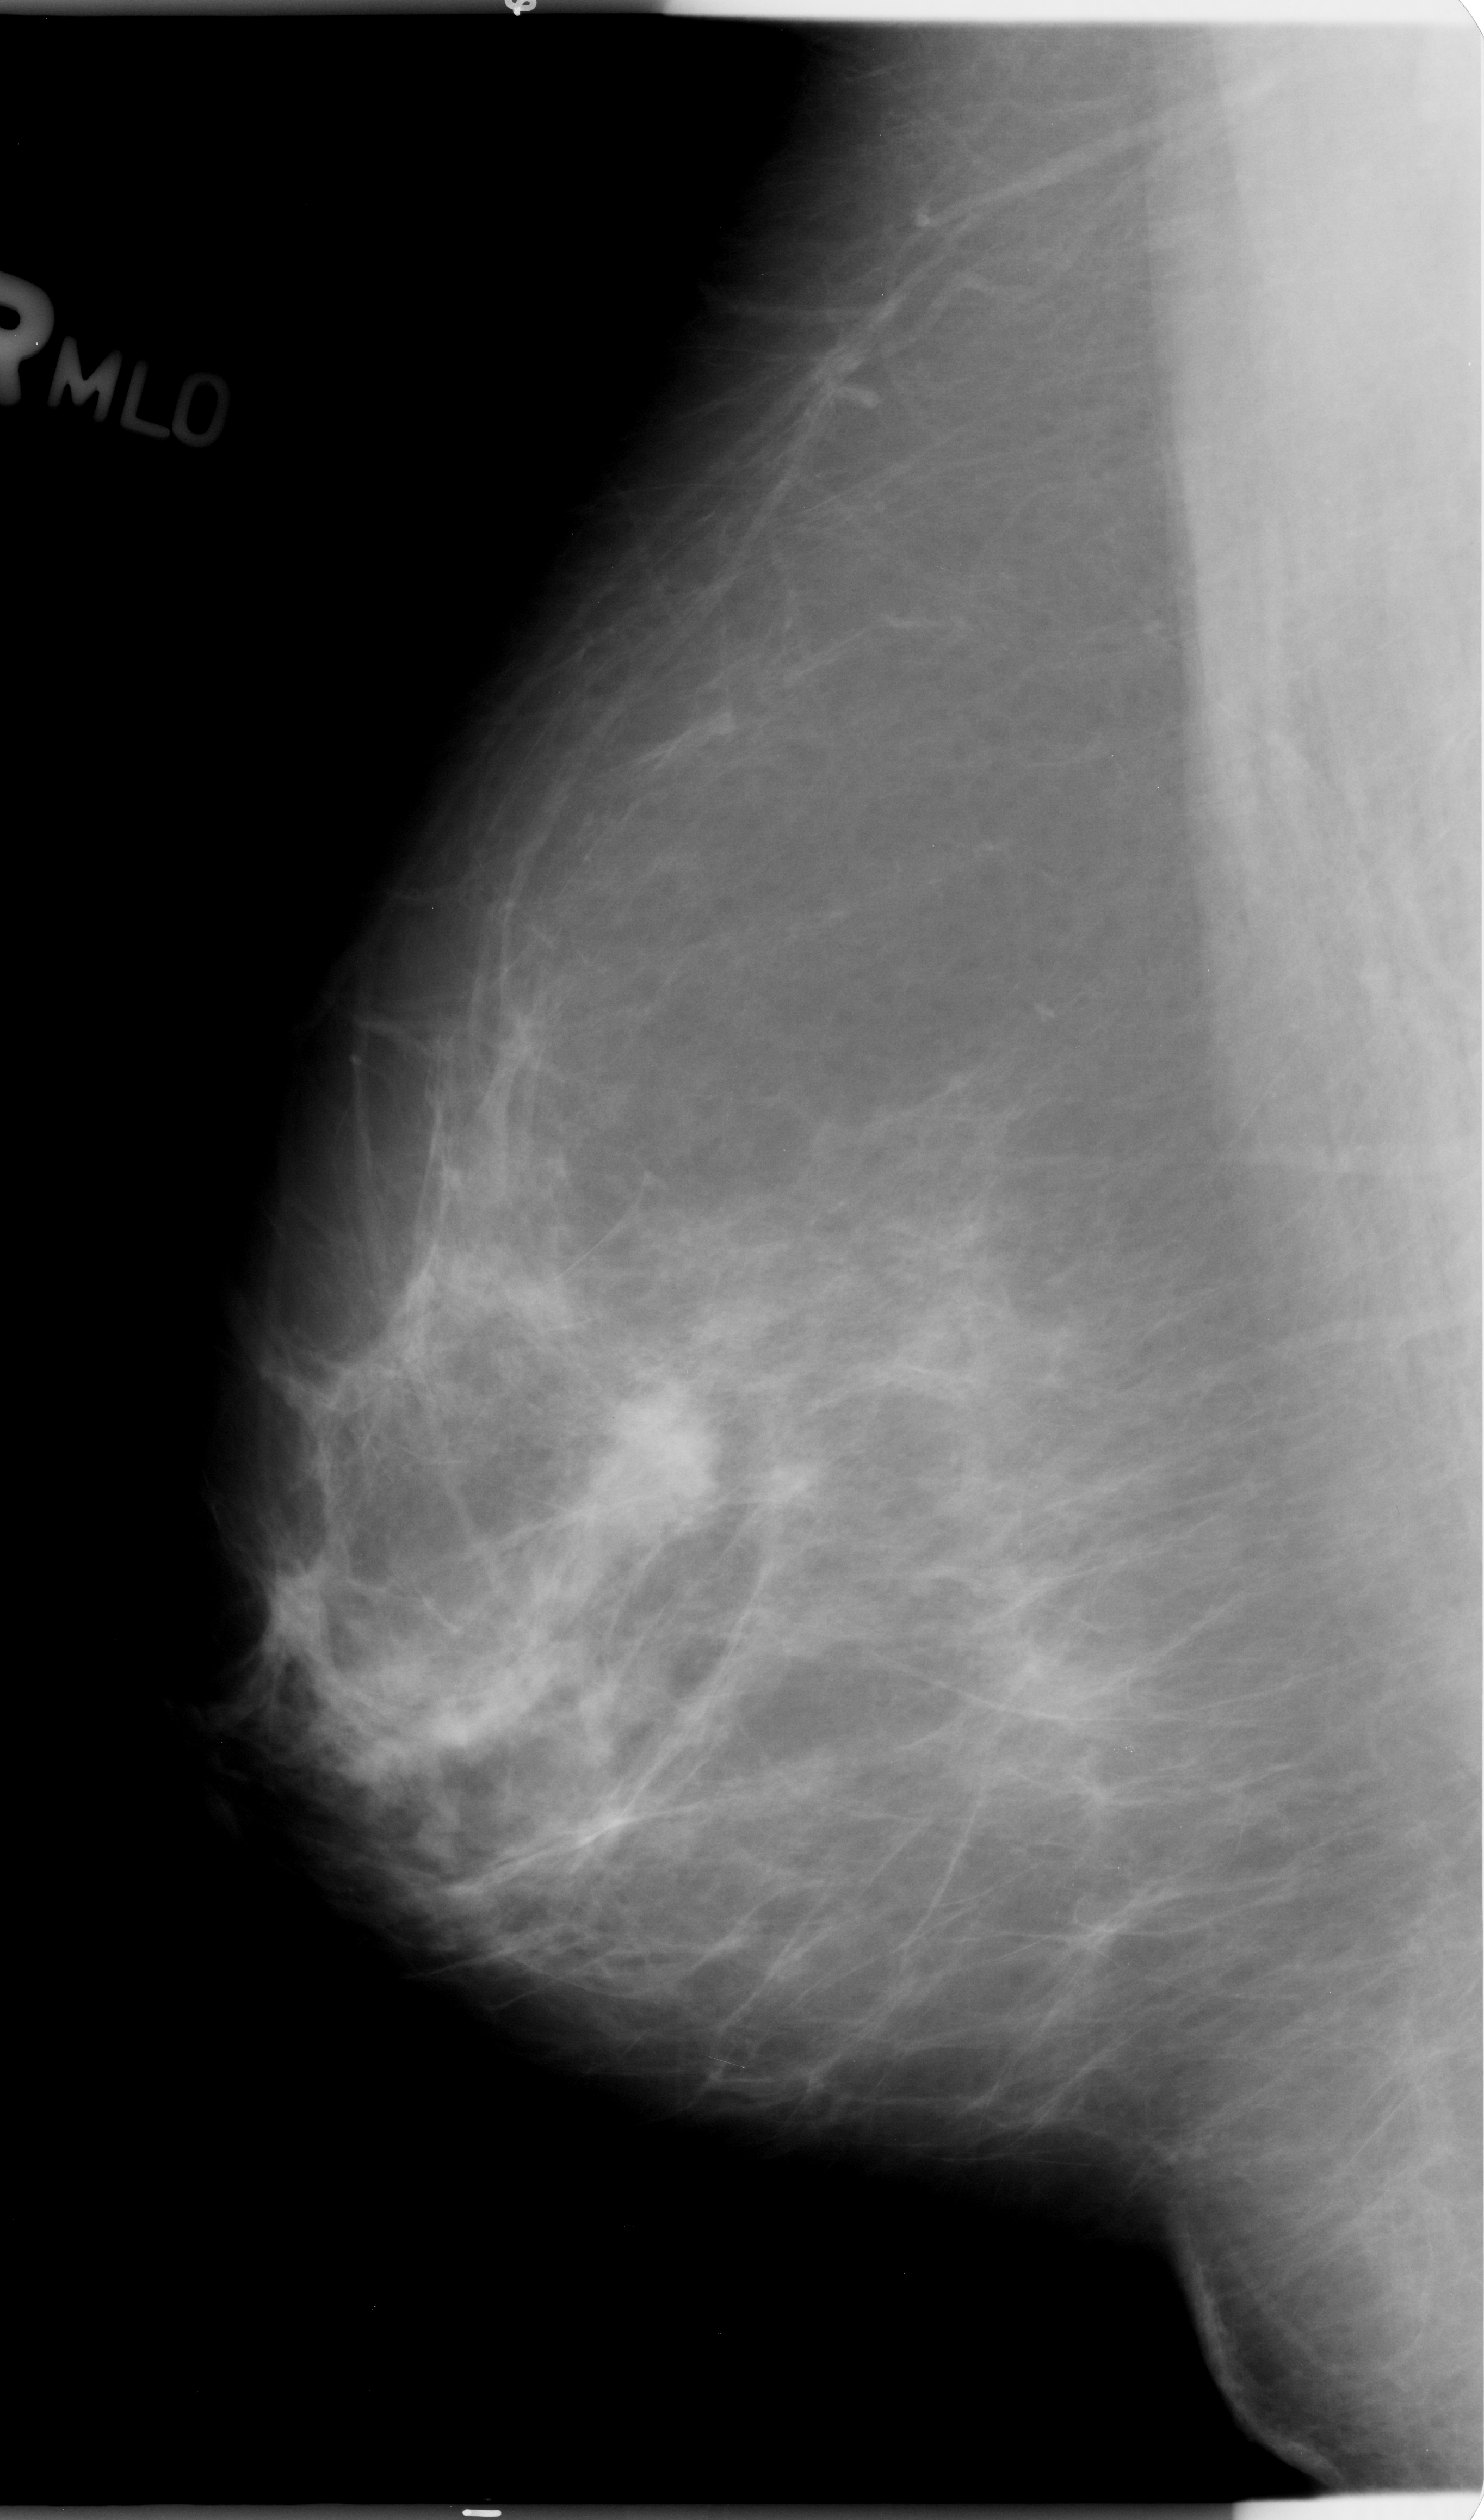
Digitized screen-film mammogram; right breast; mediolateral oblique (MLO) view; breast composition: scattered fibroglandular densities (BI-RADS density category 2 of 4).
Marked findings (only marked abnormalities are described; nothing is implied about the rest of the image): mass, shape irregular, margins microlobulated / ill defined; BI-RADS assessment category 4; subtlety rating 4 on a 1 (subtle) to 5 (obvious) scale; pathology result (as recorded, not read from the image): malignant.